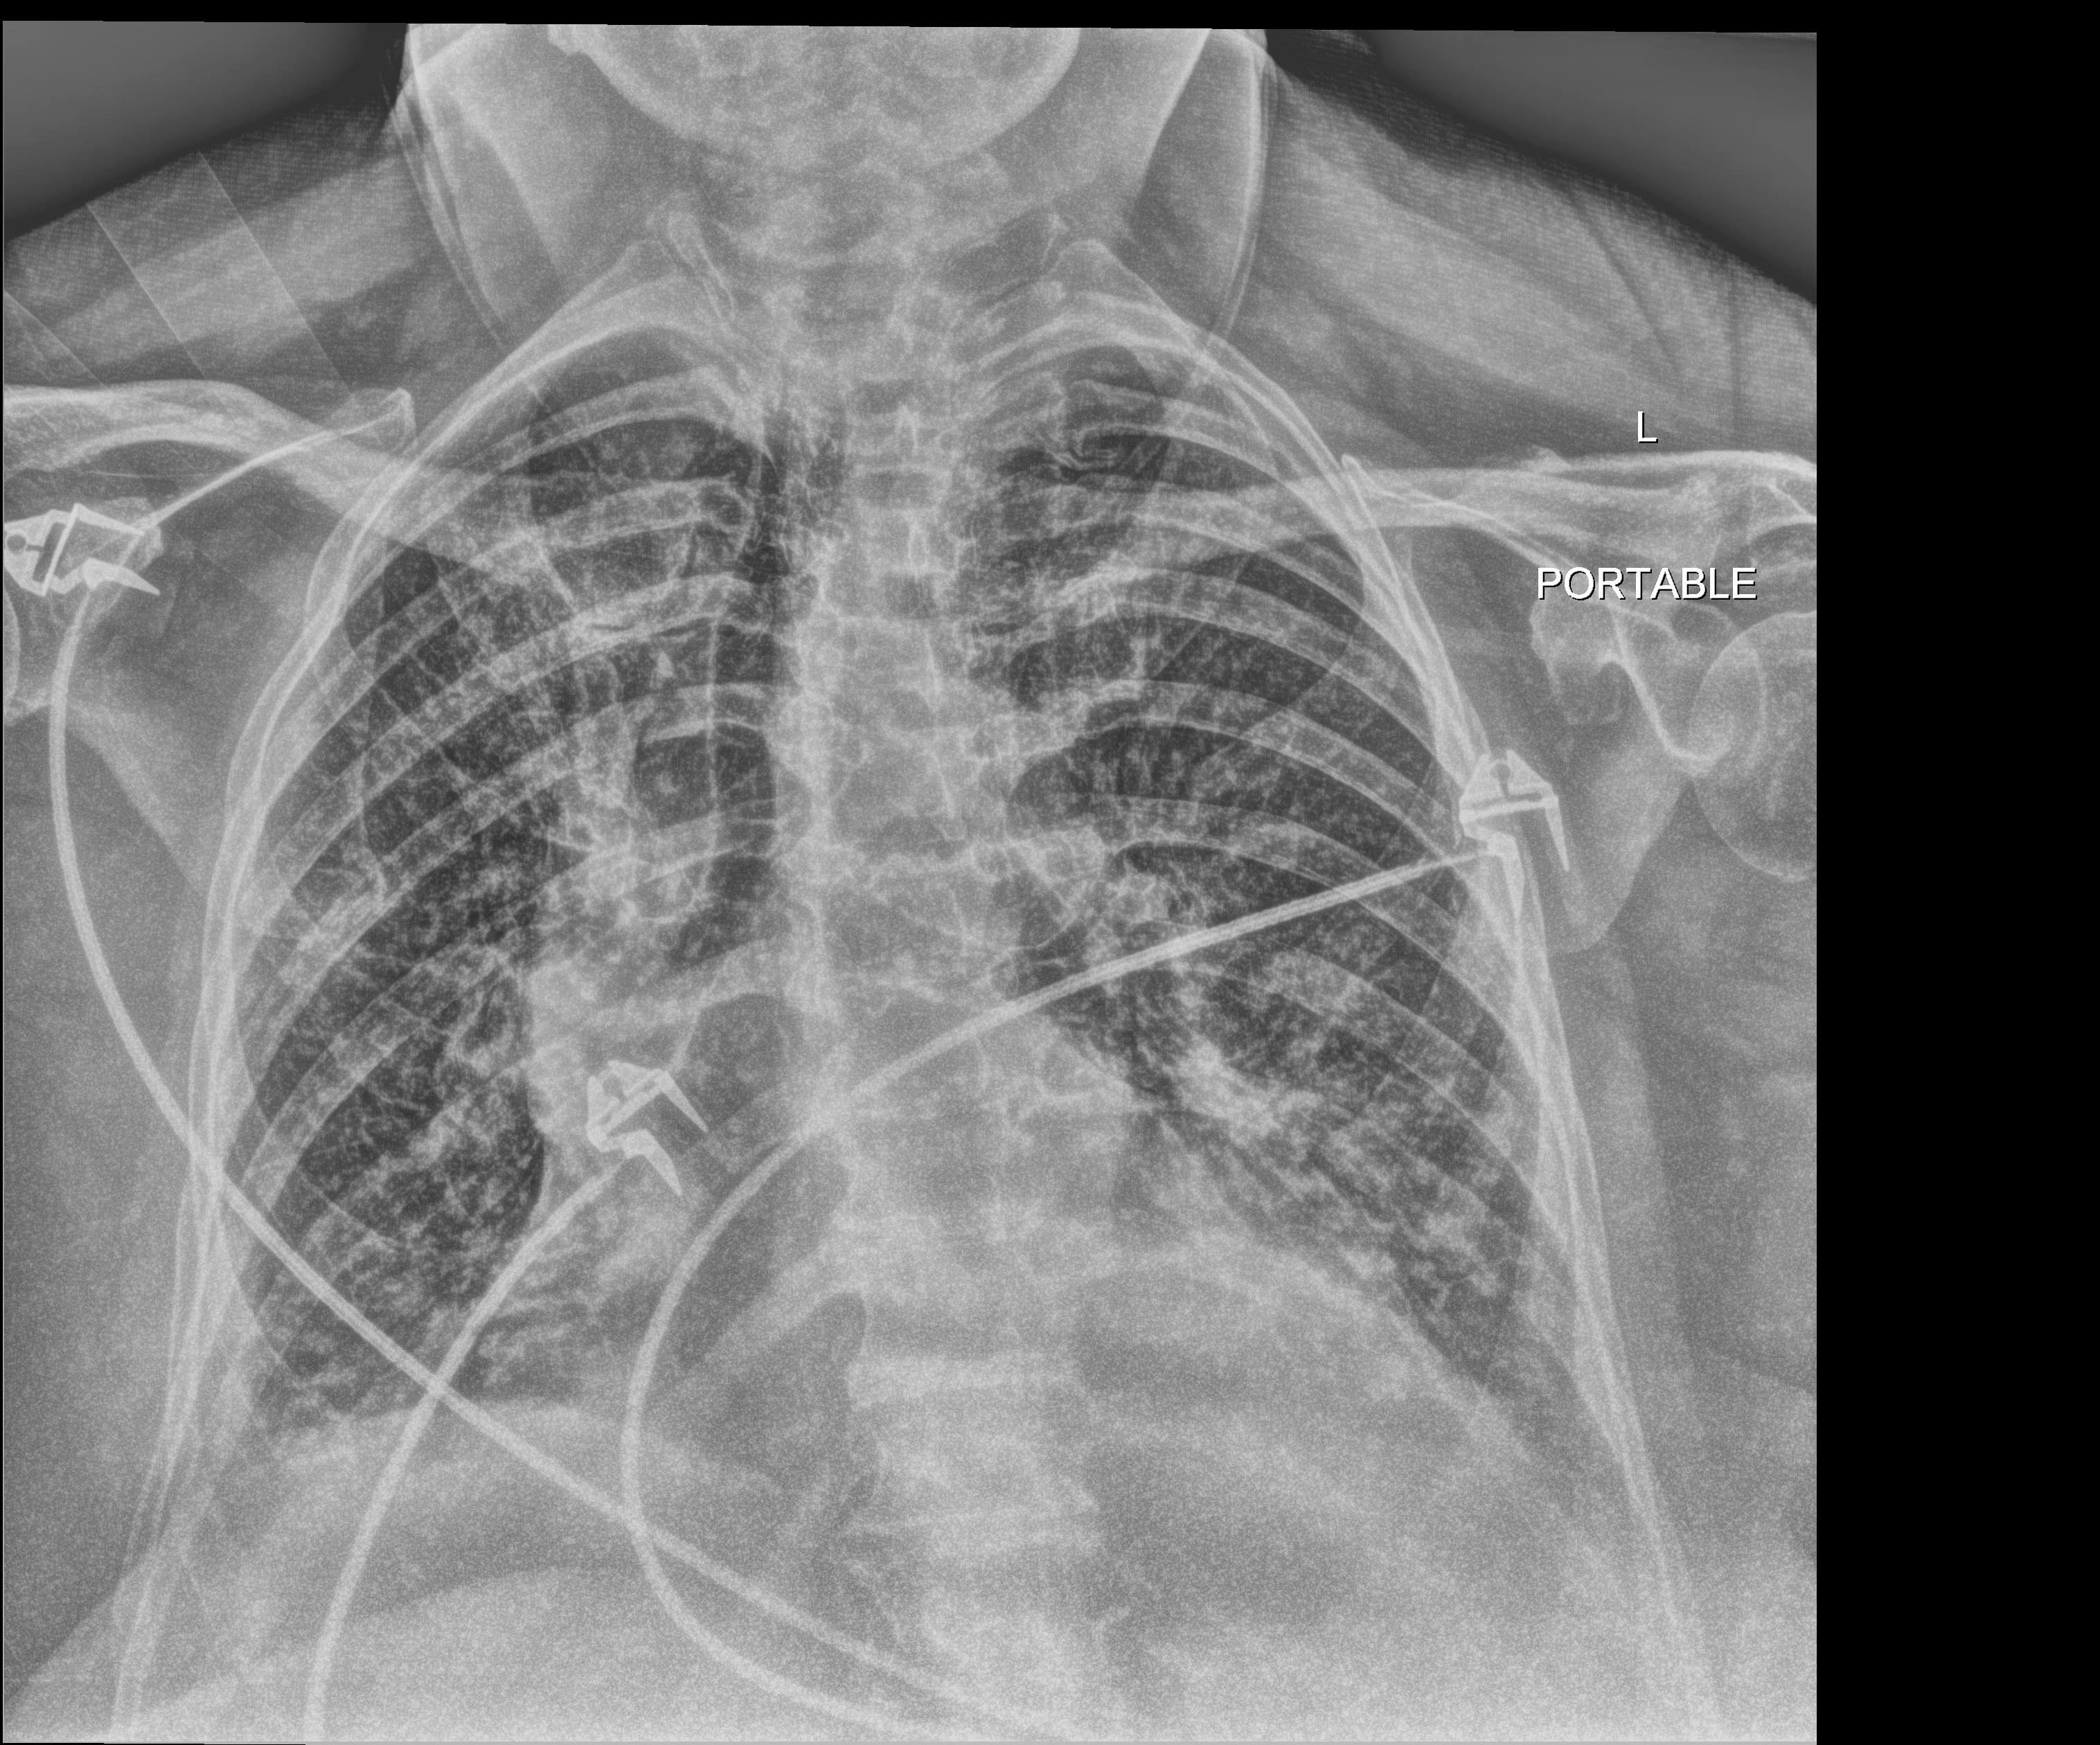
Chest X-ray, anteroposterior (AP) projection. Female patient hospitalised with COVID-19, age 75–90 years.
Admission-level facts for this patient (not findings on this image; timing relative to this image not recorded): smoking status (admission record): never.